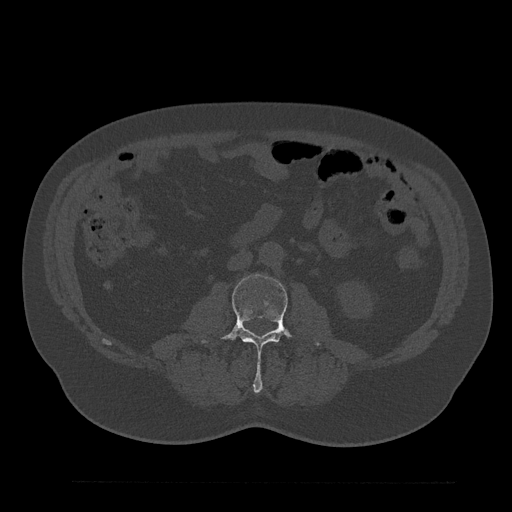
CT including the spine, one axial slice. Position 32 of 797 along the scan axis. Bone window (W 1800 / L 400 HU). 0.5 mm slice thickness. 512 × 512 image matrix, field of view 430 × 430 mm. Patient: male, 61 years. From the clinical record (not read from this slice): primary cancer: prostate.
Outlined on this slice (semi-automatically segmented with operator editing):
- L3 vertebra: bounding box <200,274,320,392> (left, top, right, bottom; pixels)